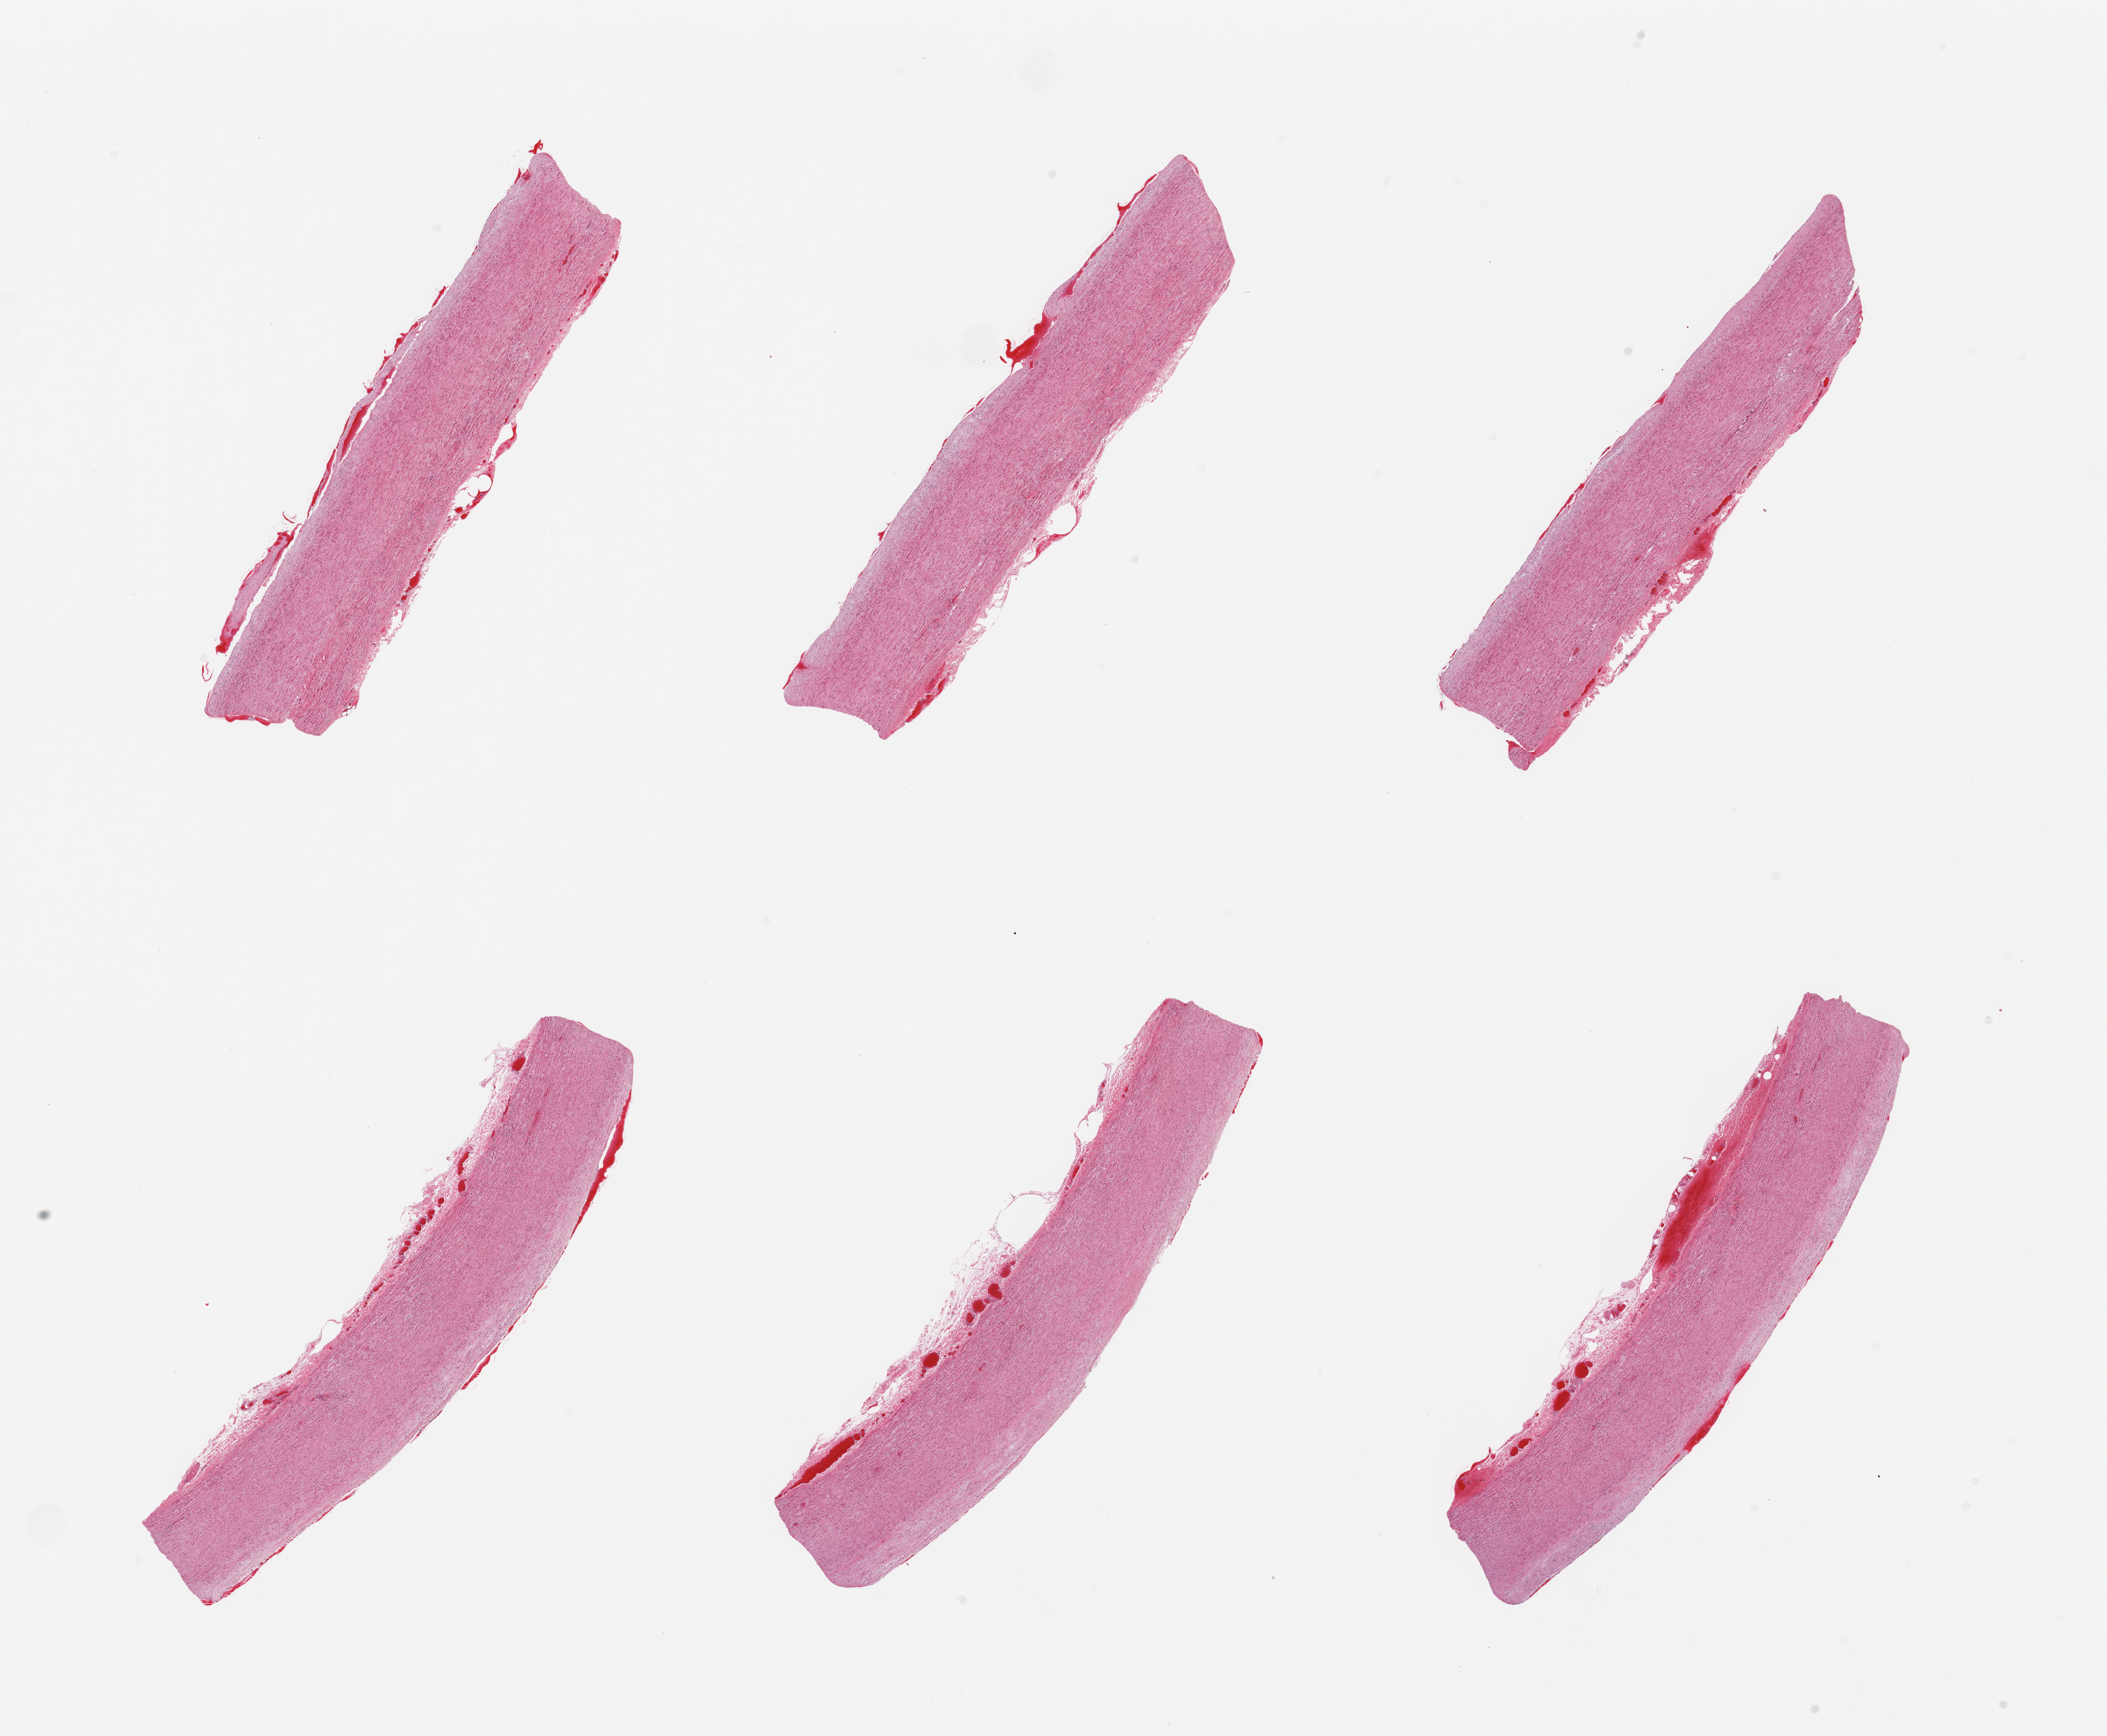
Whole-slide image, hematoxylin and eosin (H&E) stain, a low-resolution overview of the entire scanned area, about 24.6 x 20.3 mm (from a 20x scan). PAXgene-fixed paraffin-embedded (PFPE) section. Sampled site (target tissue): aorta. Donor tissue sample.
- reviewer comment on this tissue sample: 6 pieces; atherosclerosis